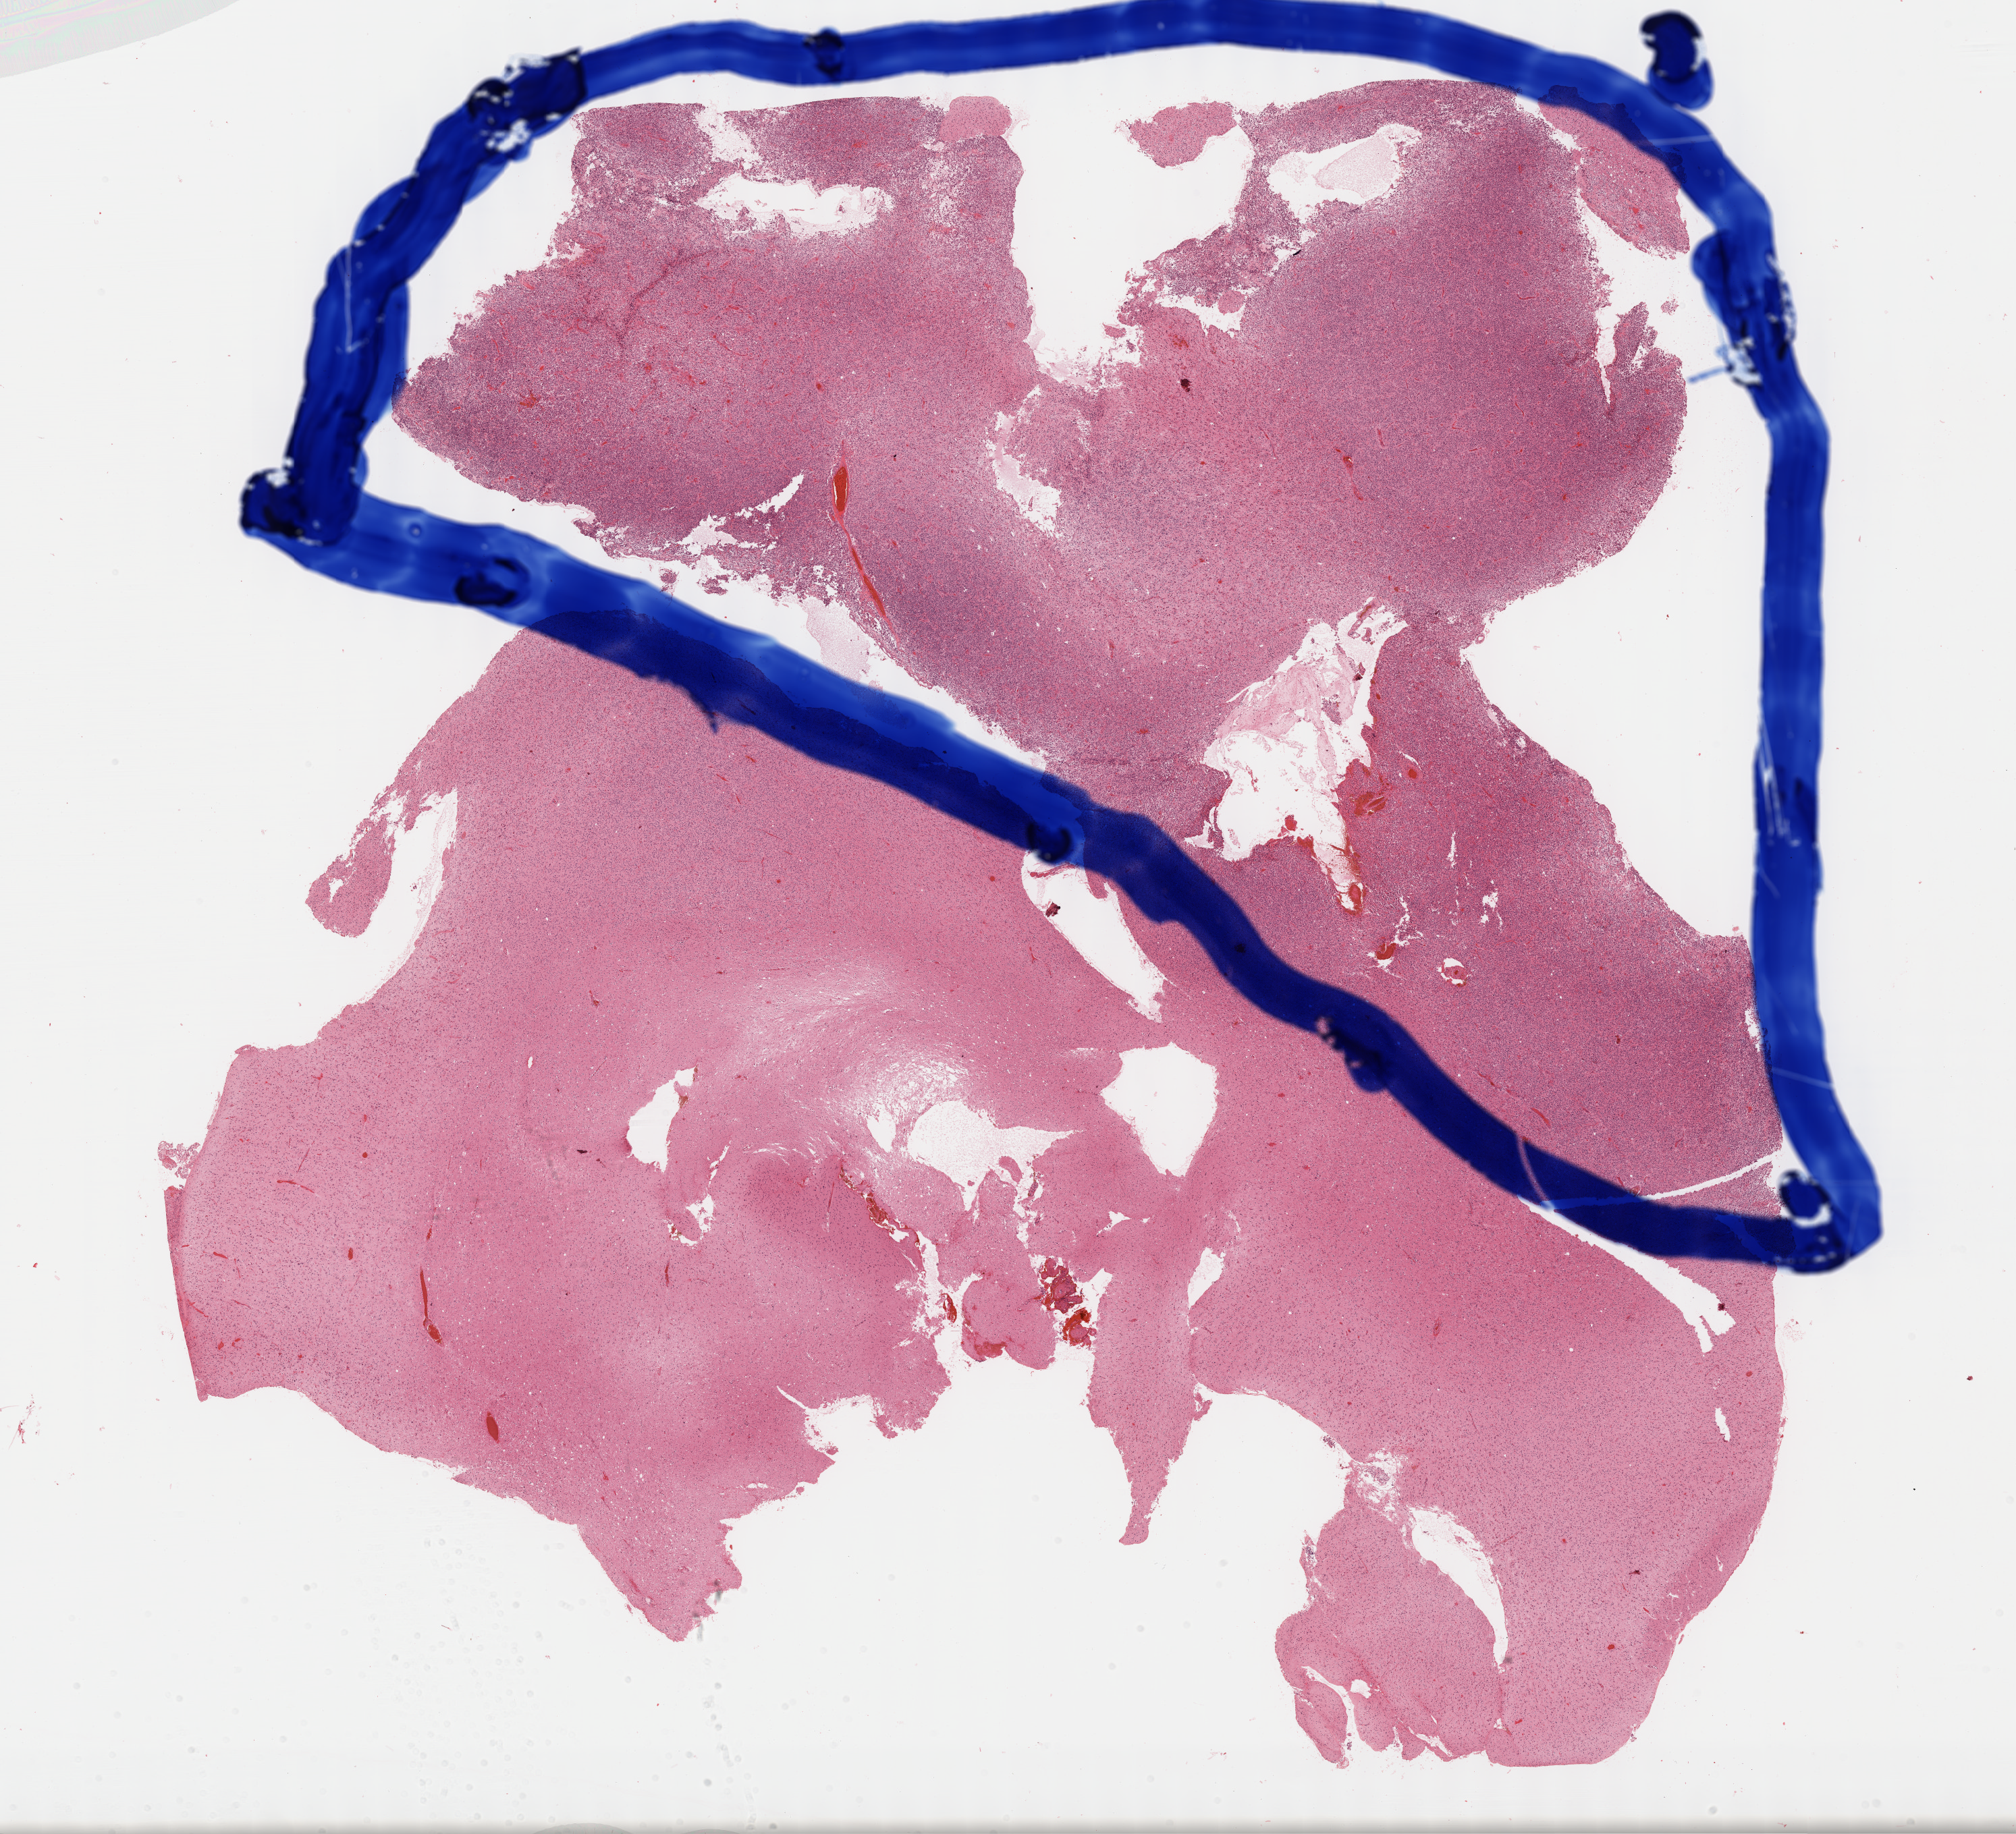
Whole-slide histology image, H&E, a low-resolution overview of the entire scanned area, about 24.2 x 22.0 mm (slide scanned at 40x). Formalin-fixed paraffin-embedded (FFPE) diagnostic section. Brain, primary tumour sample. Male, age 63 years at initial diagnosis.
Pathologic diagnosis: Oligodendroglioma, anaplastic (cerebrum).